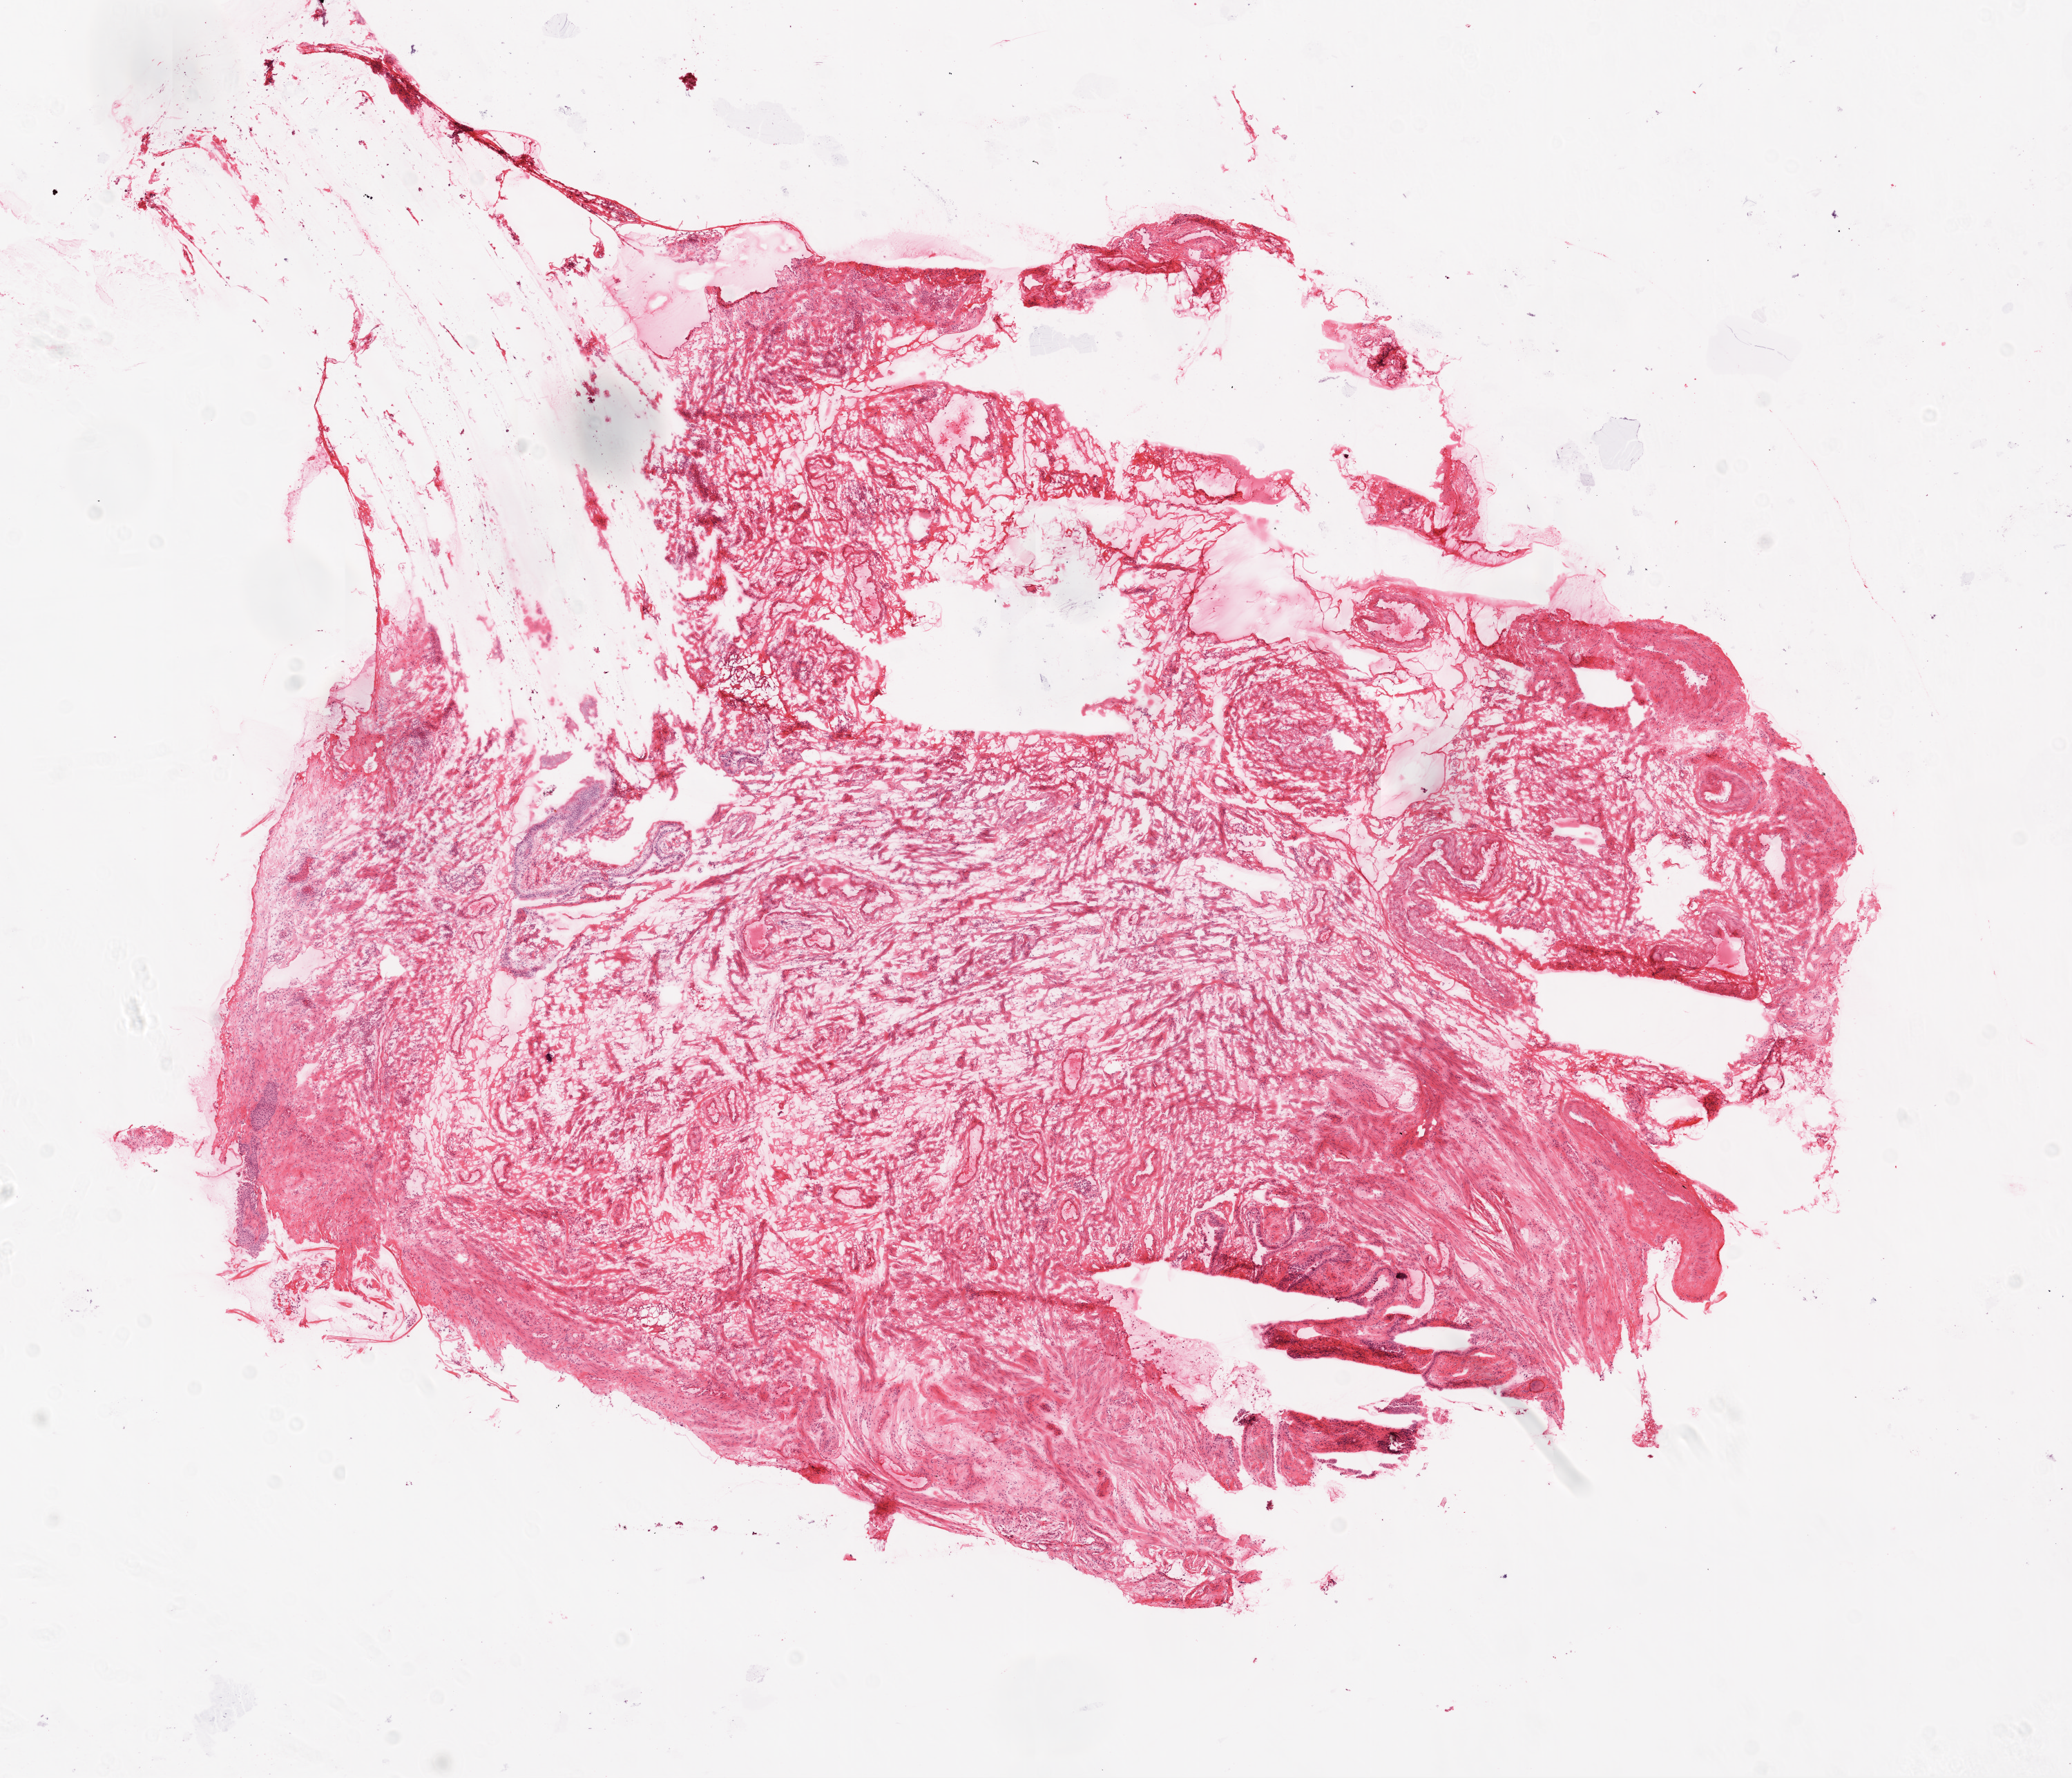
Digitized Hematoxylin and eosin (H&E) stained tissue section (whole slide) — a low-resolution overview of the entire scanned area, about 12.0 x 10.3 mm (acquisition: 20x scan); frozen section from the top of the tissue portion; solid tissue normal (non-tumour tissue) sample from the ovary. Patient: female, age at initial diagnosis 52 years.
This section: solid tissue normal (non-tumour) sample from the same patient. Patient diagnosis: Serous cystadenocarcinoma, NOS.